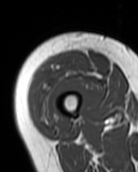
MRI of an extremity soft-tissue mass, one axial slice. Slice 23 of 99 in the series (ordered by position). MR volume resampled by the dataset authors to the PET/CT grid (not the native acquisition matrix). 3.27 mm slice thickness. 138 × 172 image matrix, field of view 135 × 168 mm. Female patient. Case-level facts recorded for this patient, not image findings: histological type: pleiomorphic undifferentiated sarcoma; grade: high; site of the primary tumour: right quadricep.
Annotated regions visible in this slice (expert contour drawn on MRI and transferred to this co-registered scan by the dataset authors):
- gross tumour volume including surrounding oedema: bounding box [x1, y1, x2, y2] px = [32, 57, 90, 122]